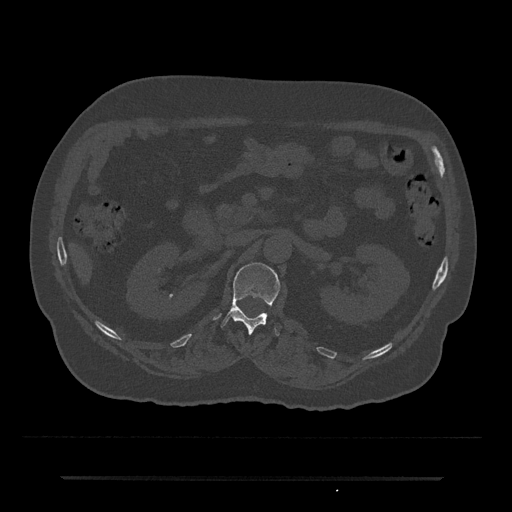
CT including the spine, one axial slice. Slice 70 of 797 in the series (ordered by position). Reconstruction kernel Br40s/3. Bone window (W 1800 / L 400 HU). 0.5 mm slice thickness. 512 × 512 image matrix, field of view 437 × 437 mm. Patient: male, 69 years. Case-level facts recorded for this patient, not image findings: primary cancer: prostate.
Outlined on this slice (semi-automatic segmentation, software-assisted and operator-edited):
- L1 vertebra: bounding box <221,262,280,336> (left, top, right, bottom; pixels)